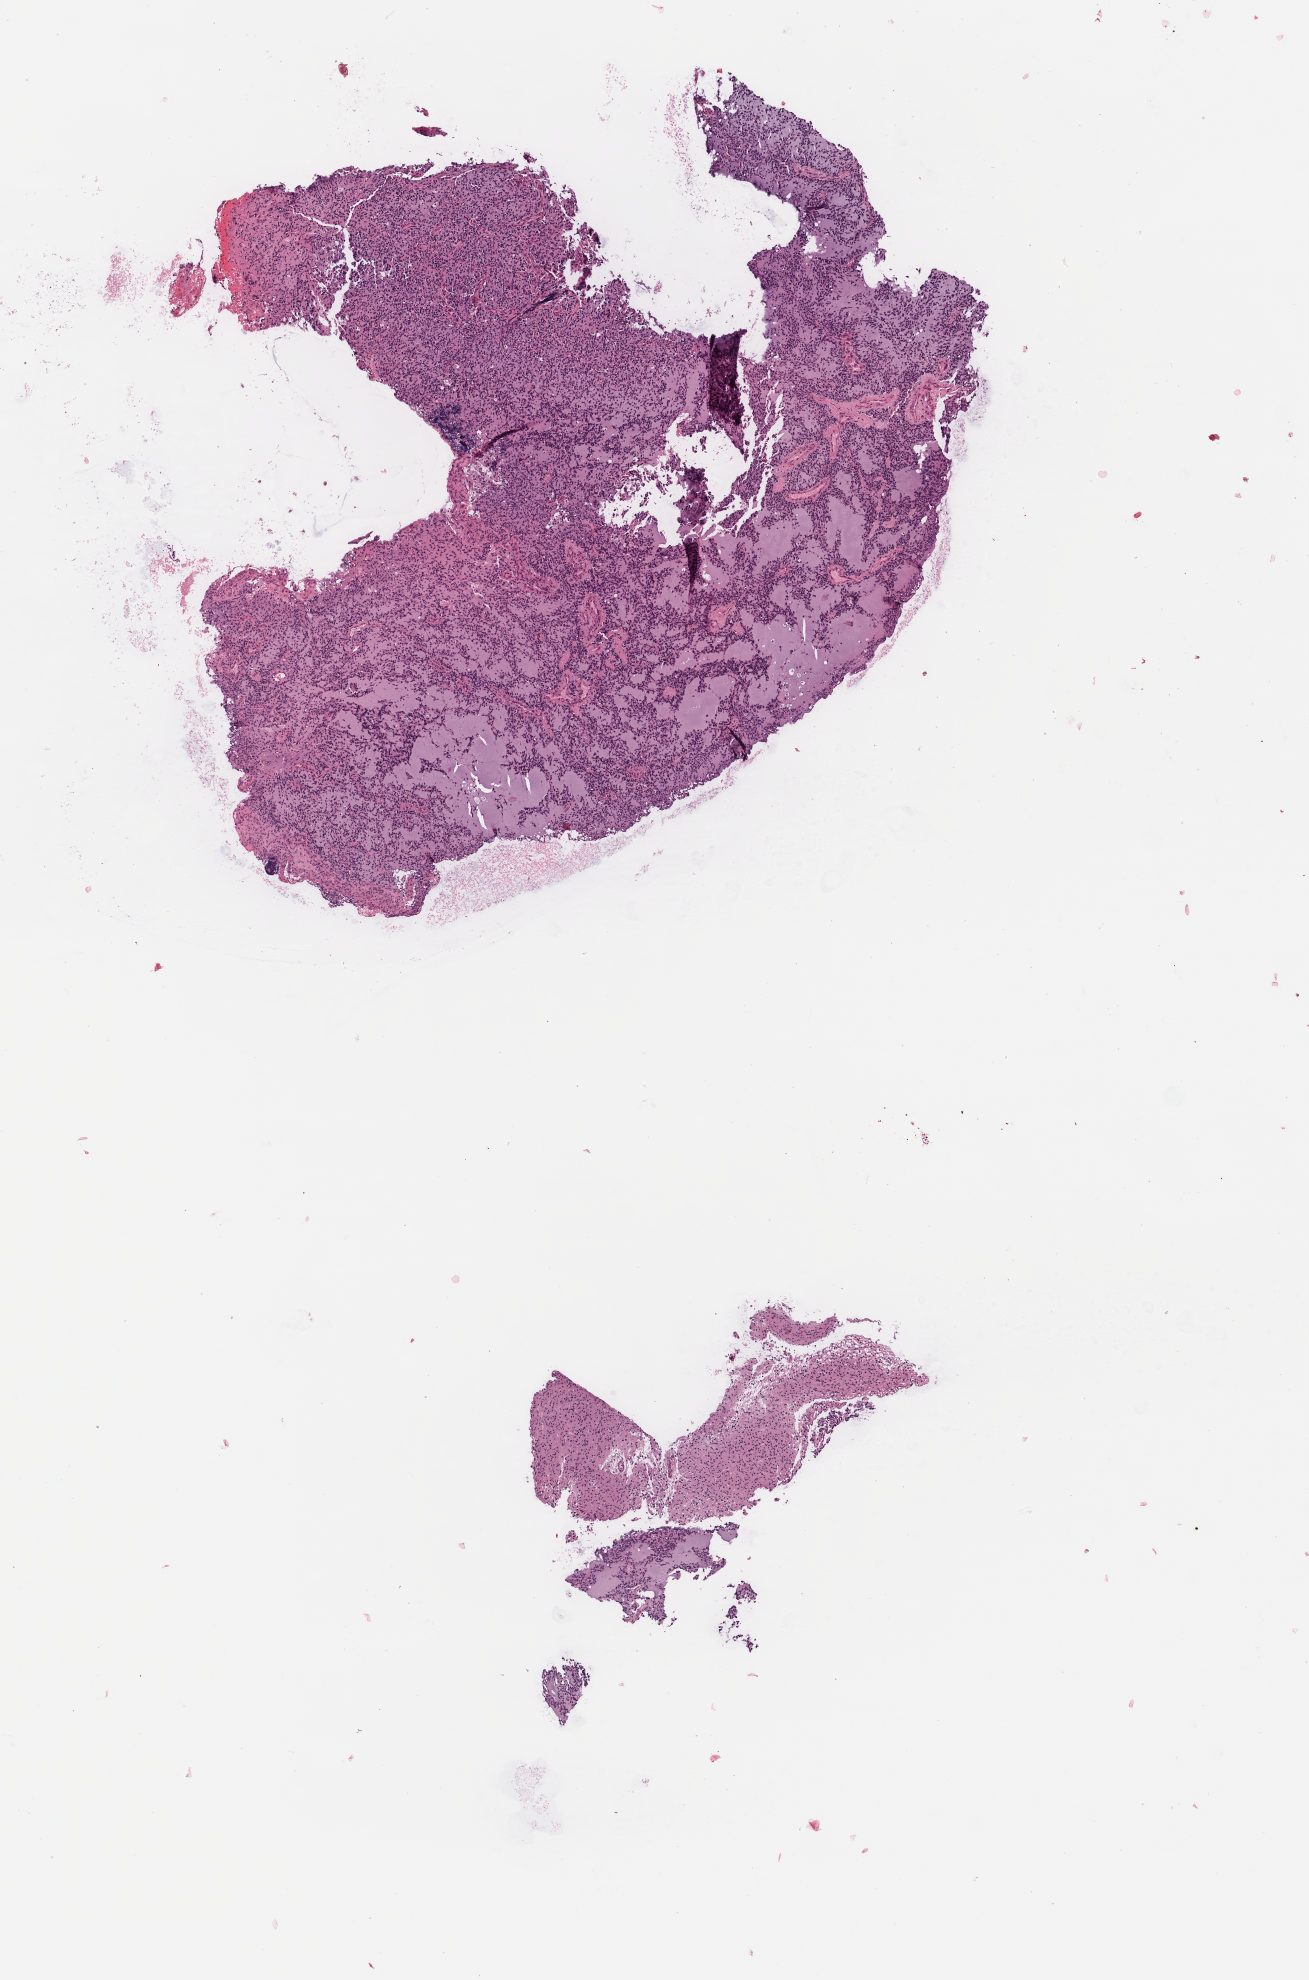
Digitized H&E tissue section (whole slide), a low-resolution overview of the entire scanned area, about 5.1 x 7.8 mm (slide scanned at 40x); formalin-fixed paraffin-embedded (FFPE) diagnostic section; primary tumour sample from the brain. Male, age 30 years at initial diagnosis. Histologic grade: G3 (poorly differentiated).
Histologic diagnosis: Oligodendroglioma, anaplastic (cerebrum).